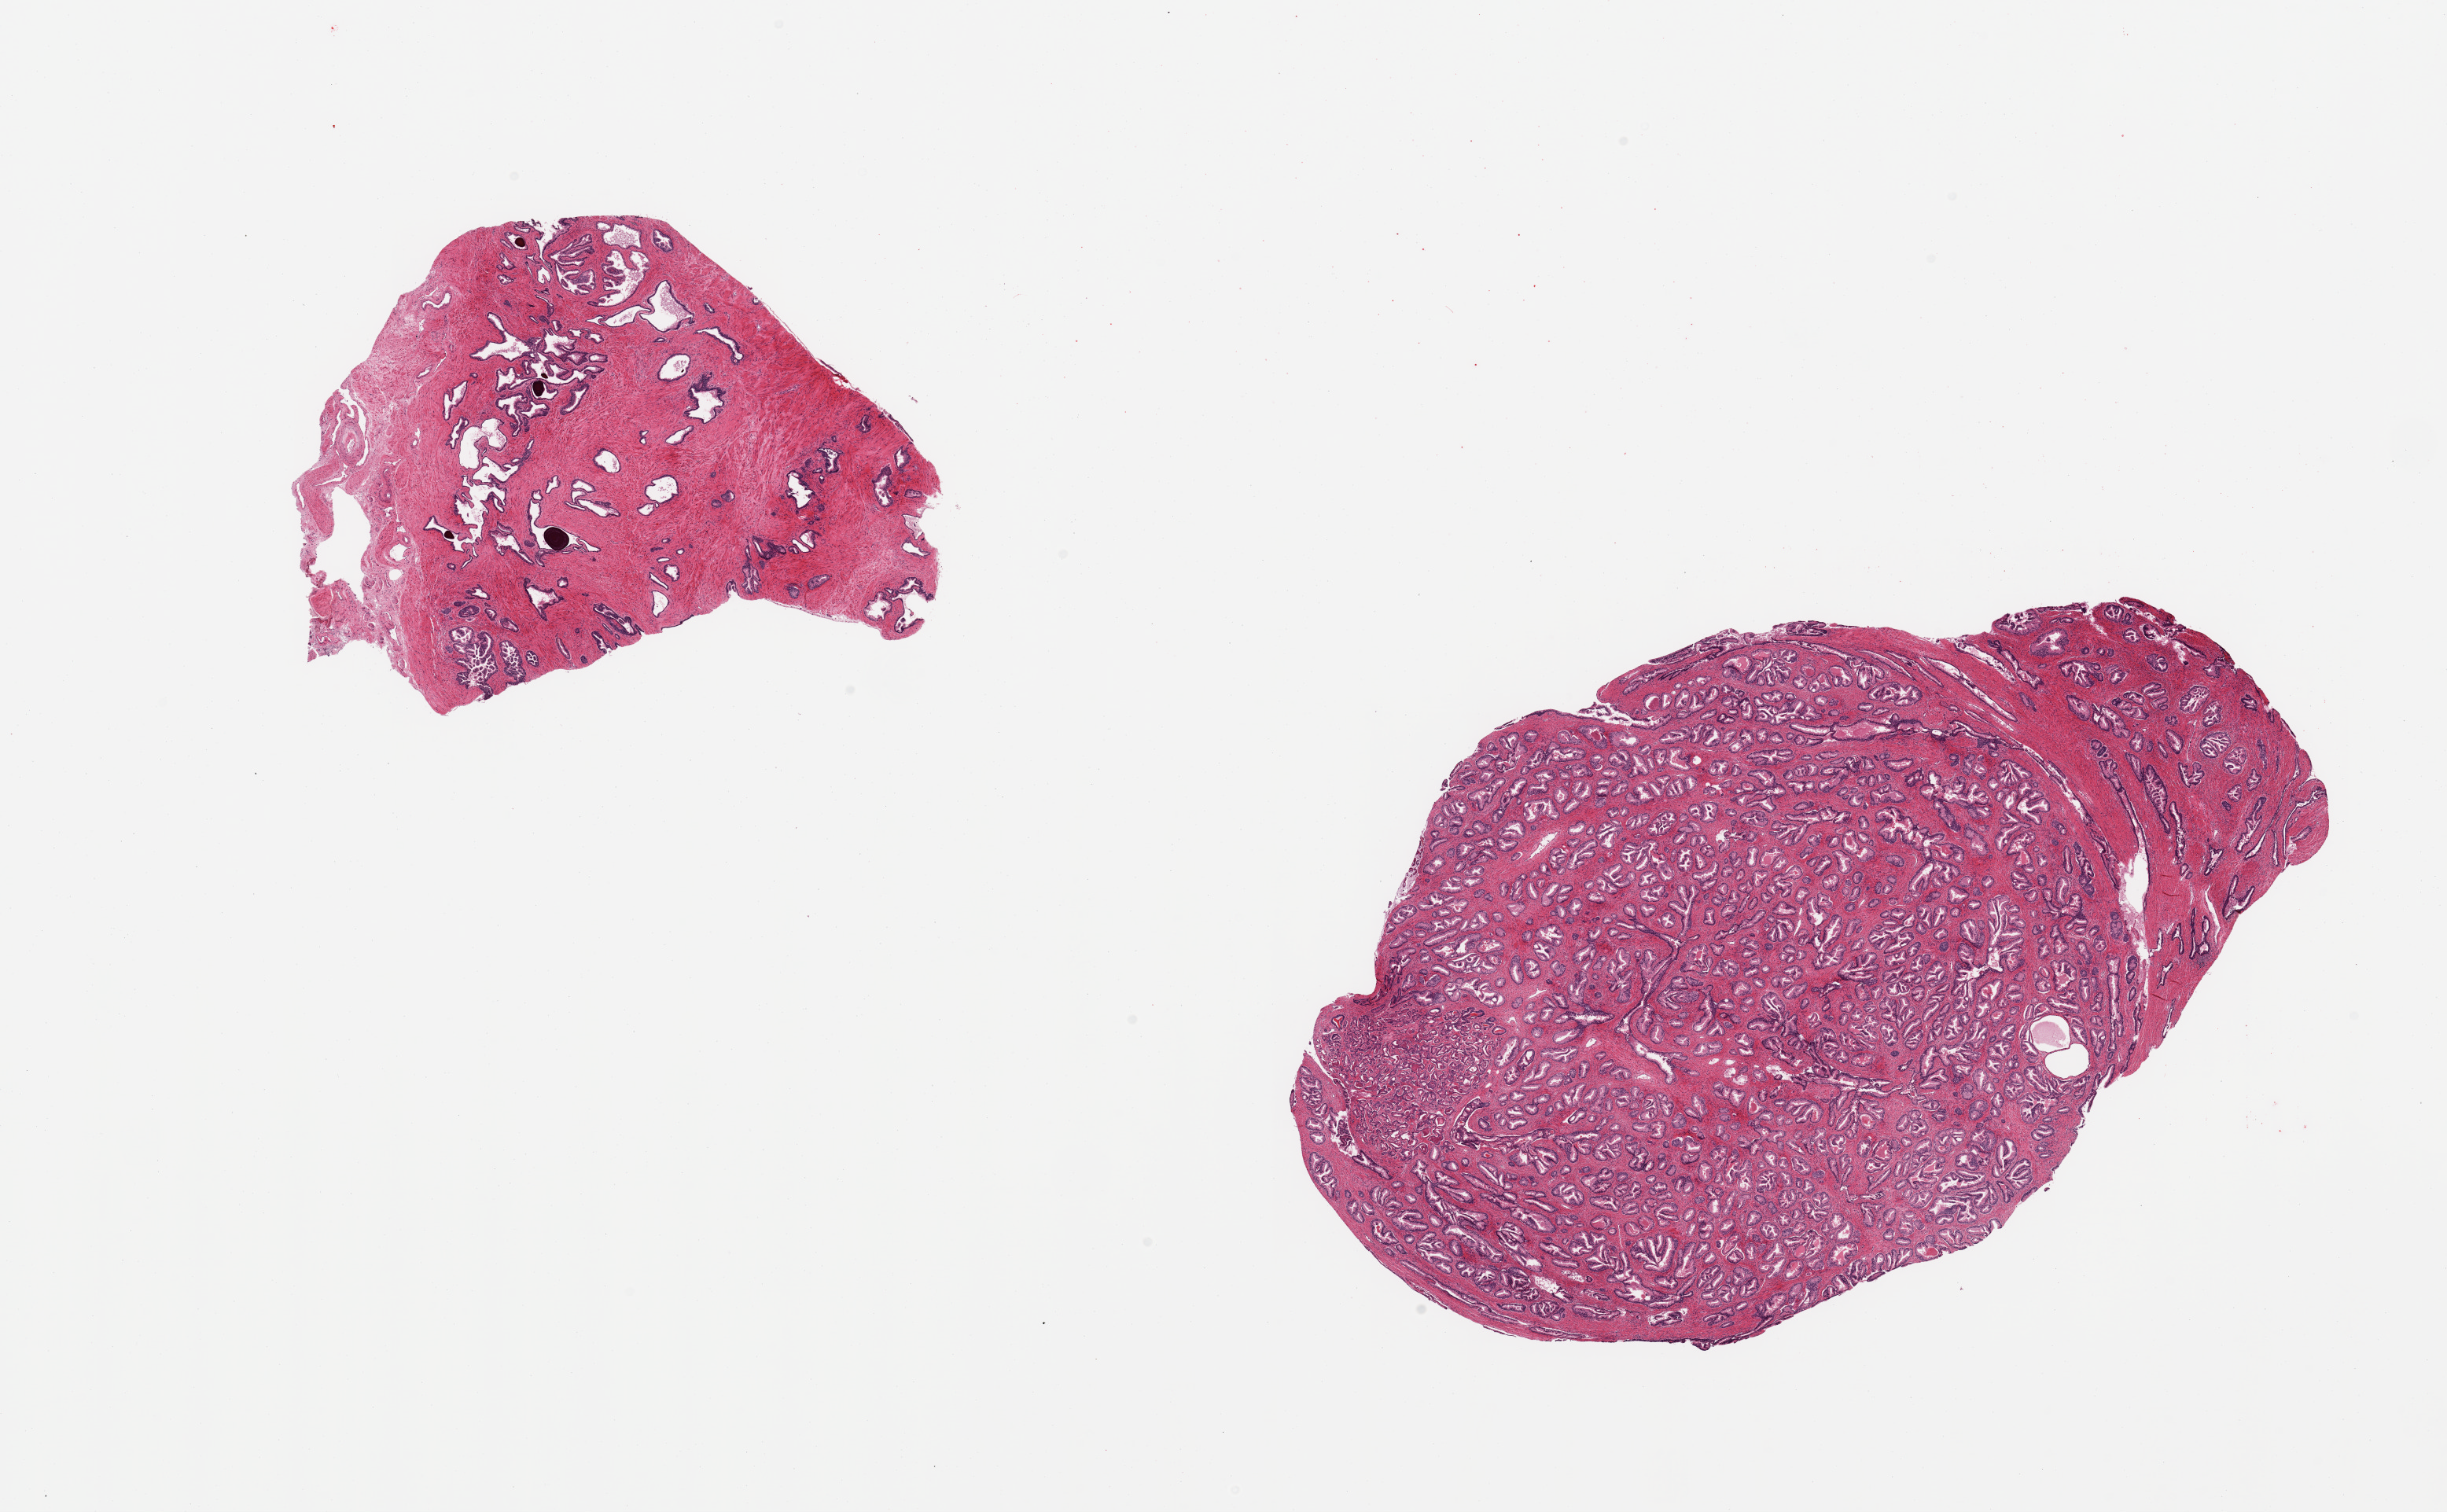
Whole-slide image, haematoxylin and eosin stain, shown as a low-resolution overview of the whole scanned area (about 24.6 x 15.2 mm, slide scanned at 20x); PAXgene-fixed paraffin-embedded (PFPE) section; section of prostate (target tissue); donor tissue sample. Donor sex: male.
Review note (as recorded): 2 pieces; focus of adenocarcinoma, Gleason score 4+3=7.